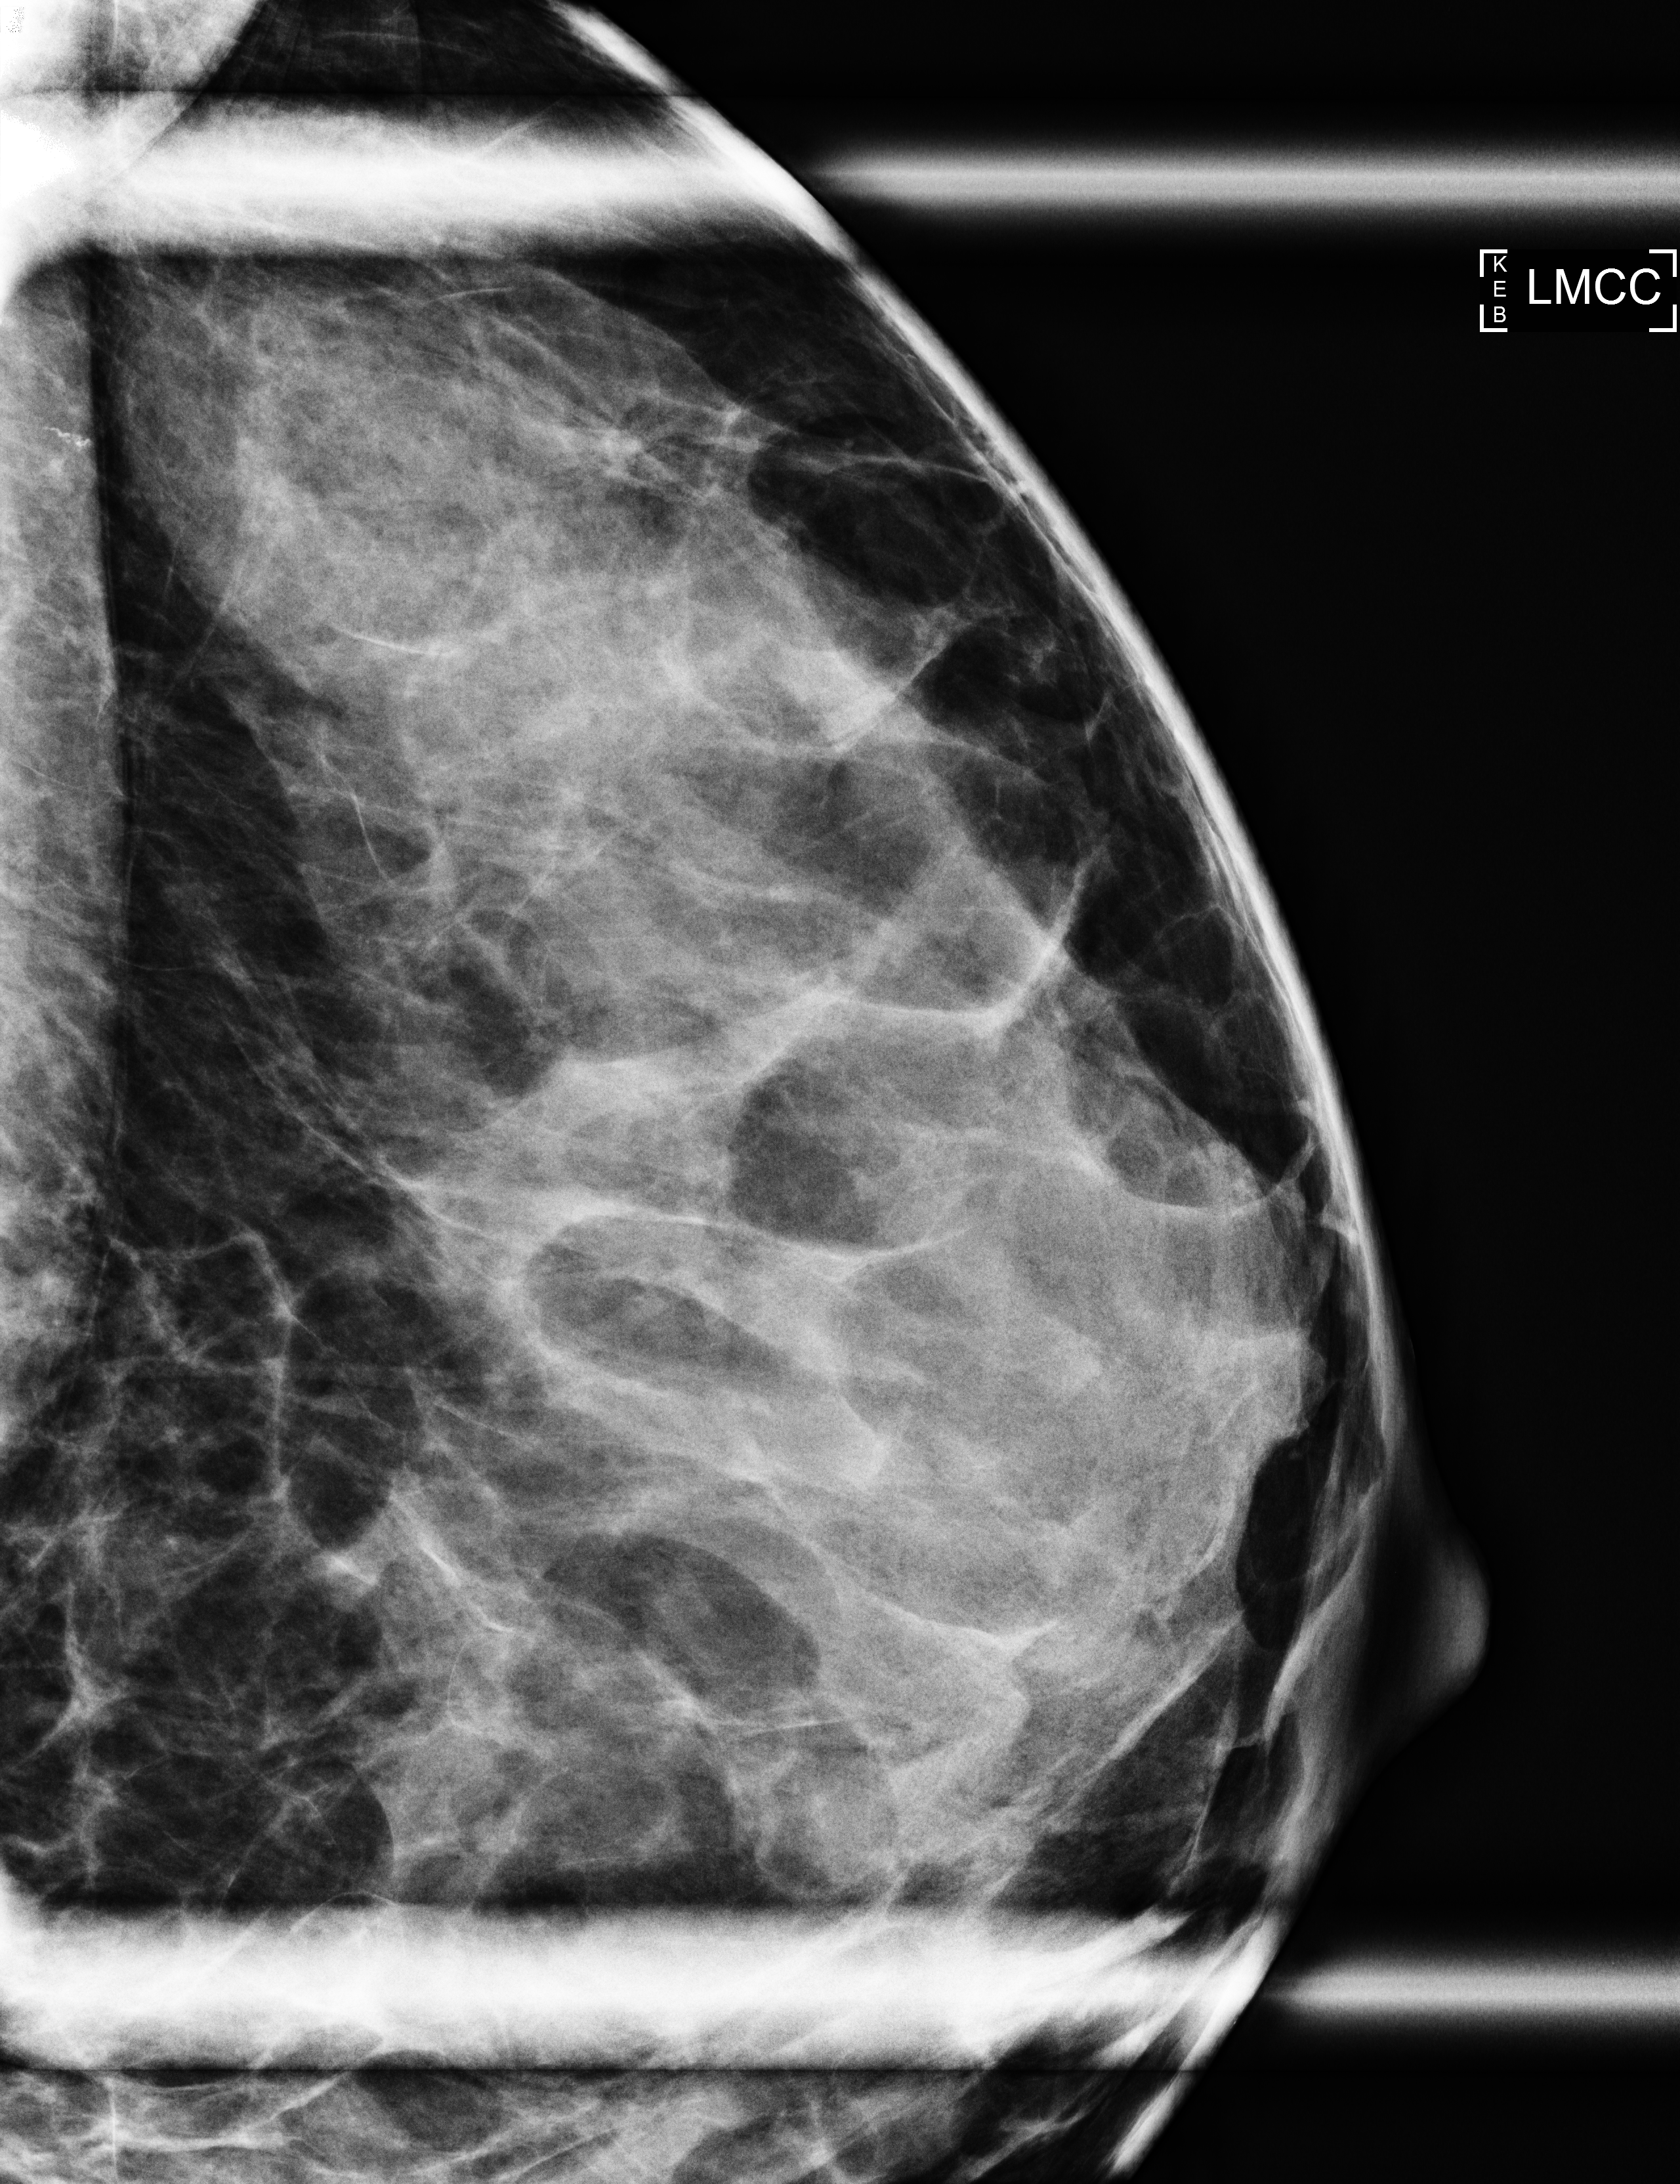
Additional (diagnostic) view. Patient aged 56 years (female).
Image type: full-field digital mammogram. Breast: left. Projection: CC view, magnification.